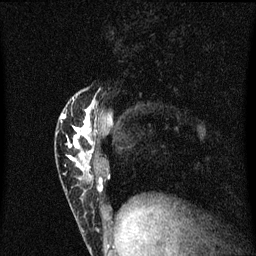
Breast MRI (dynamic contrast-enhanced), one sagittal slice. Slice 18 of 60 in the series (ordered by position). Dynamic contrast-enhanced series, image 2 of 3 at this slice position (ordered by acquisition). 1.5 T. TE 4.2 ms, TR 8.4 ms. 2 mm slice thickness. 256 × 256 image matrix, field of view 200 × 200 mm. Female patient, age 40 years.
Annotated regions visible in this slice (semi-automatic segmentation, software-assisted and operator-edited):
- analysis volume of interest (the breast-tissue region the enhancement analysis was run in; not a lesion): bounding box (x1, y1, x2, y2) in pixels: (57, 90, 104, 201)
- tumour enhancement mask (voxels above the 70 % enhancement threshold inside the analysis volume of interest): (62, 98, 101, 189)